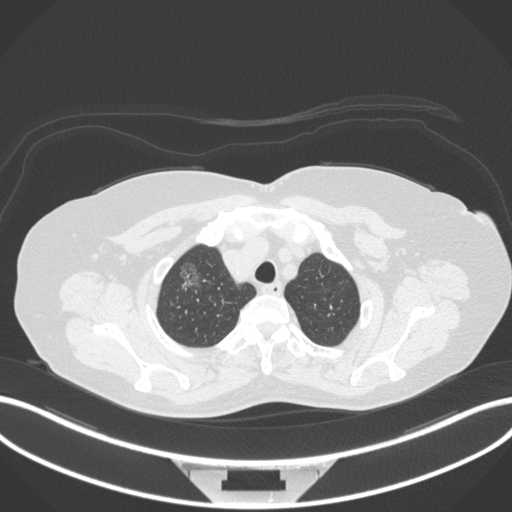
Chest CT, one axial slice. Reconstruction kernel B31f. 120 kVp. Lung window (W 1500 / L -600 HU). 1 mm slice thickness. 512 × 512 image matrix, field of view 400 × 400 mm. Female patient, age 62 years. From the clinical record (not read from this slice): clinical TNM (as recorded): T1c N0 M0.
Structures marked on this image (bounding box drawn by a radiologist):
- lung tumour (recorded histology: adenocarcinoma): box from (x=176, y=256) to (x=209, y=299) px